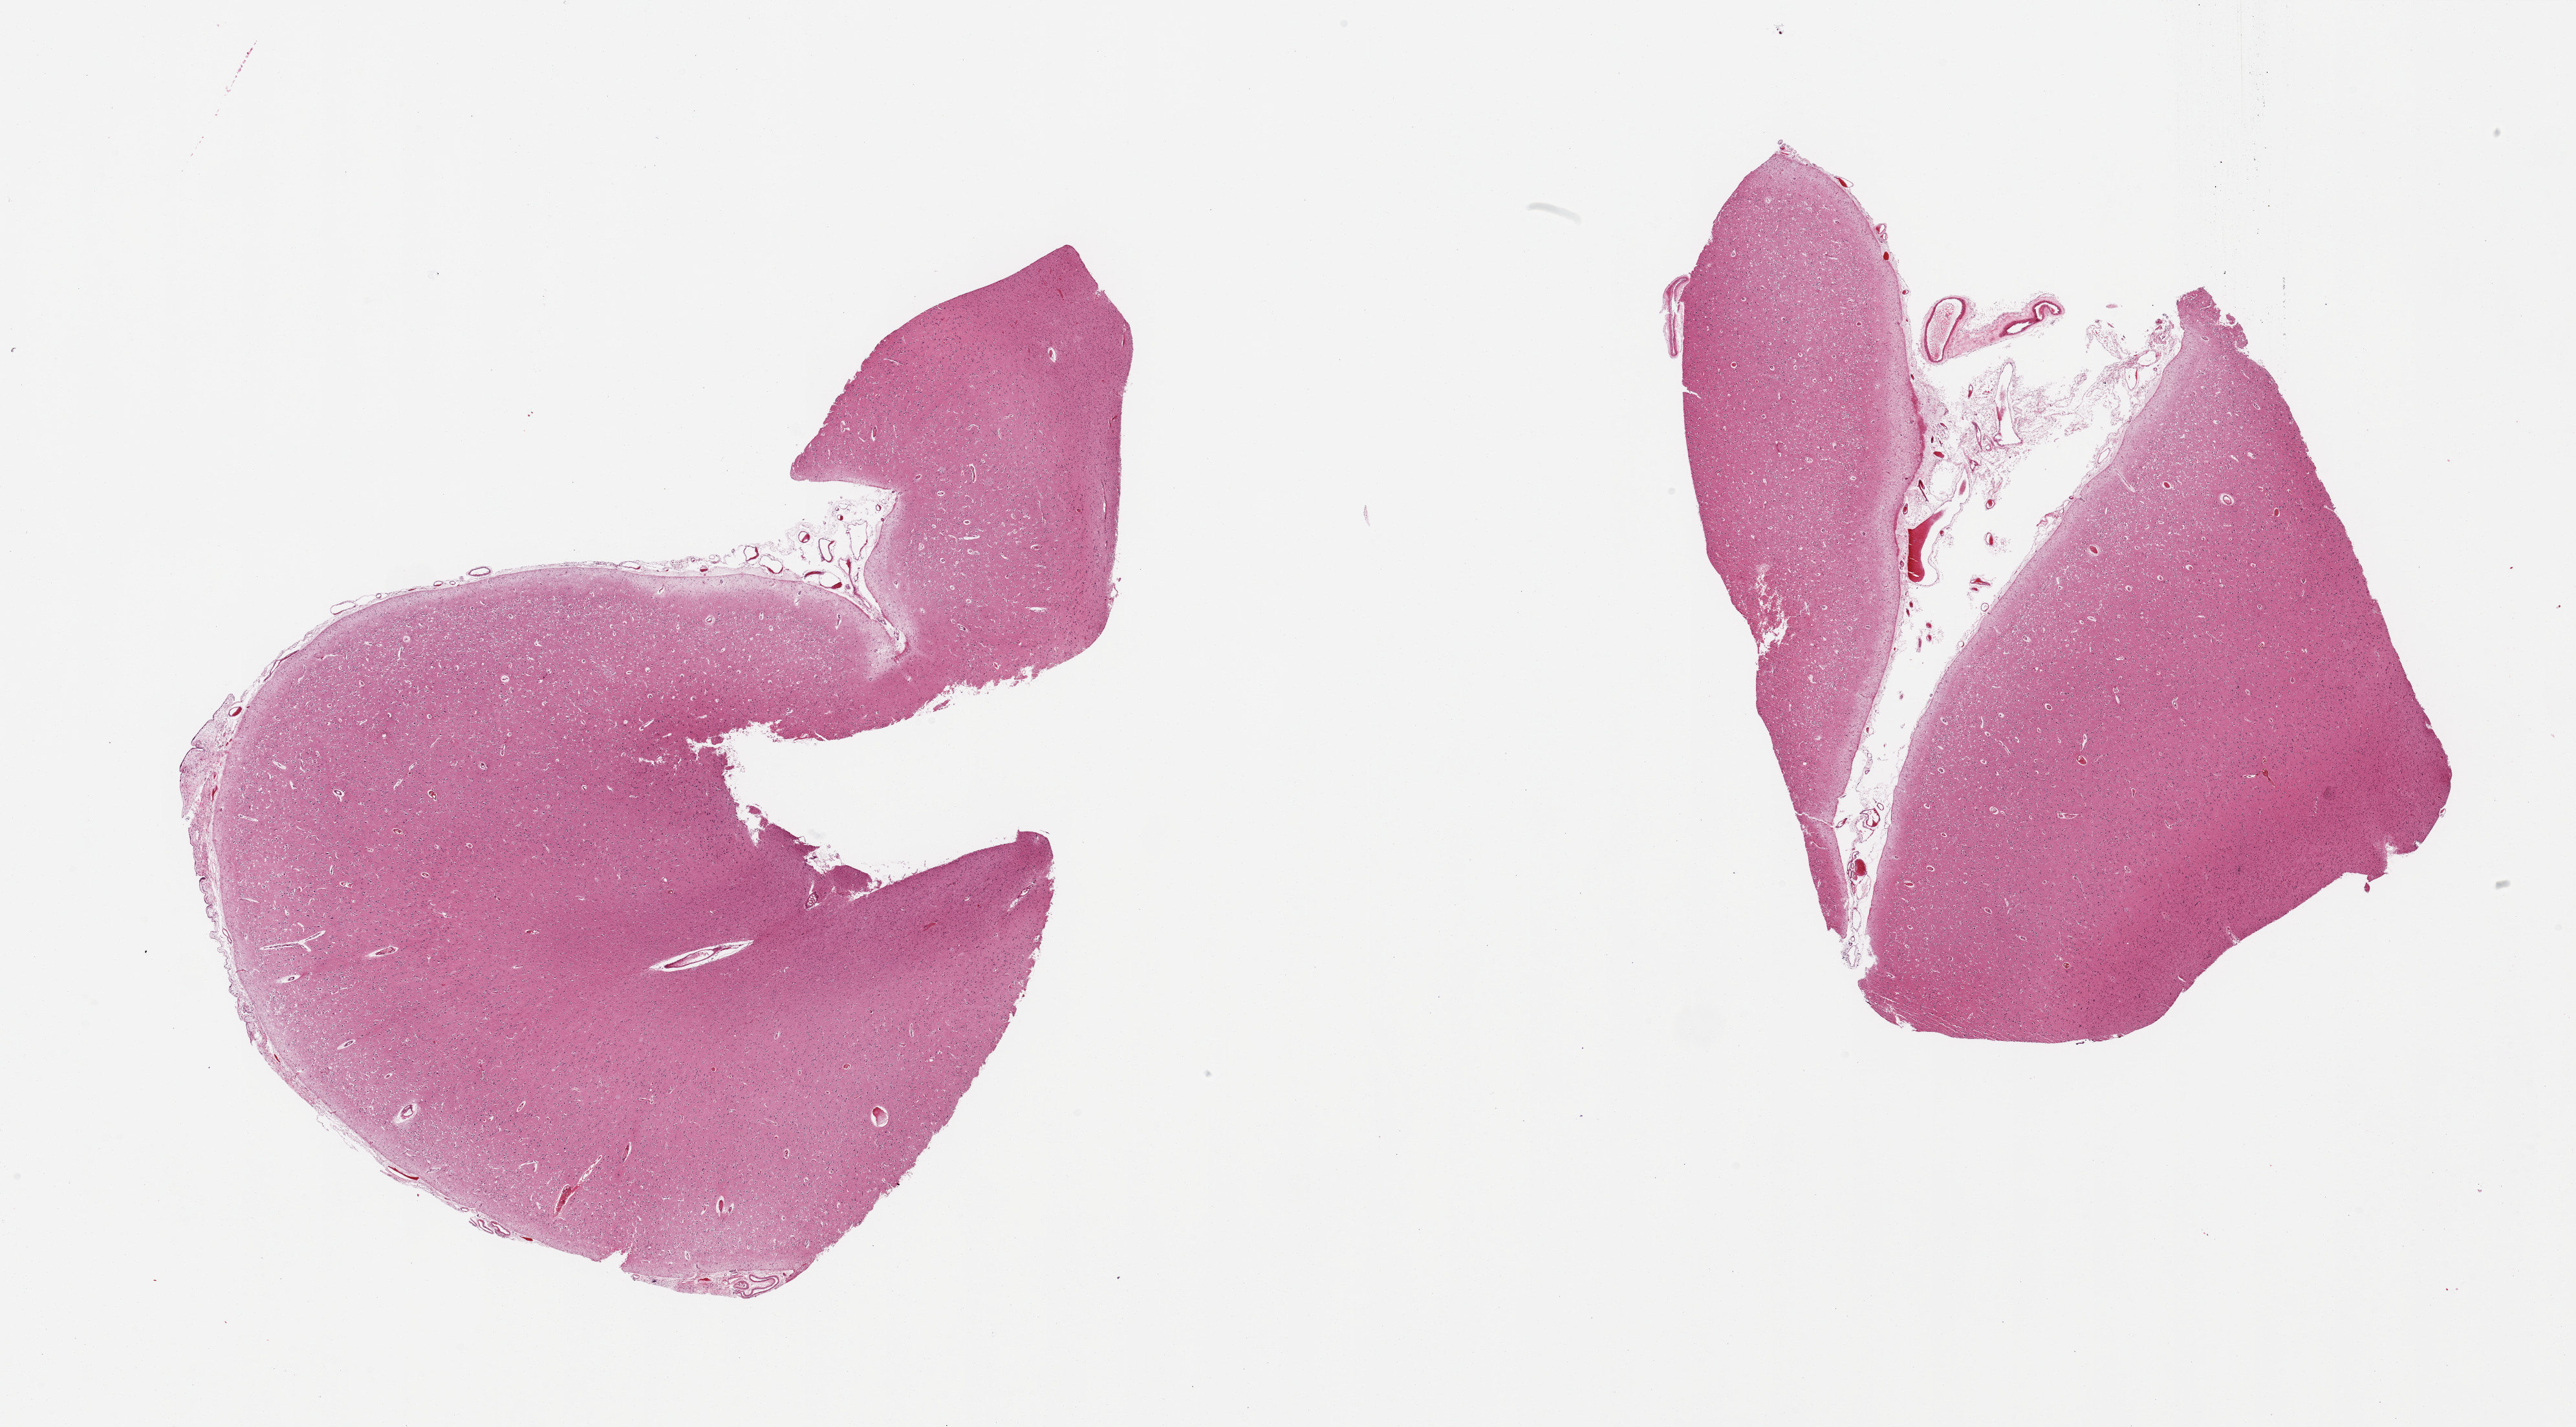
Whole-slide image, hematoxylin and eosin (H&E) stain — a low-resolution overview of the entire scanned area, about 31.5 x 17.5 mm, PAXgene-fixed, paraffin-embedded tissue, sampled site (target tissue): cerebral cortex, donor tissue sample. Donor sex: male.
• review note (as recorded): 2 pieces